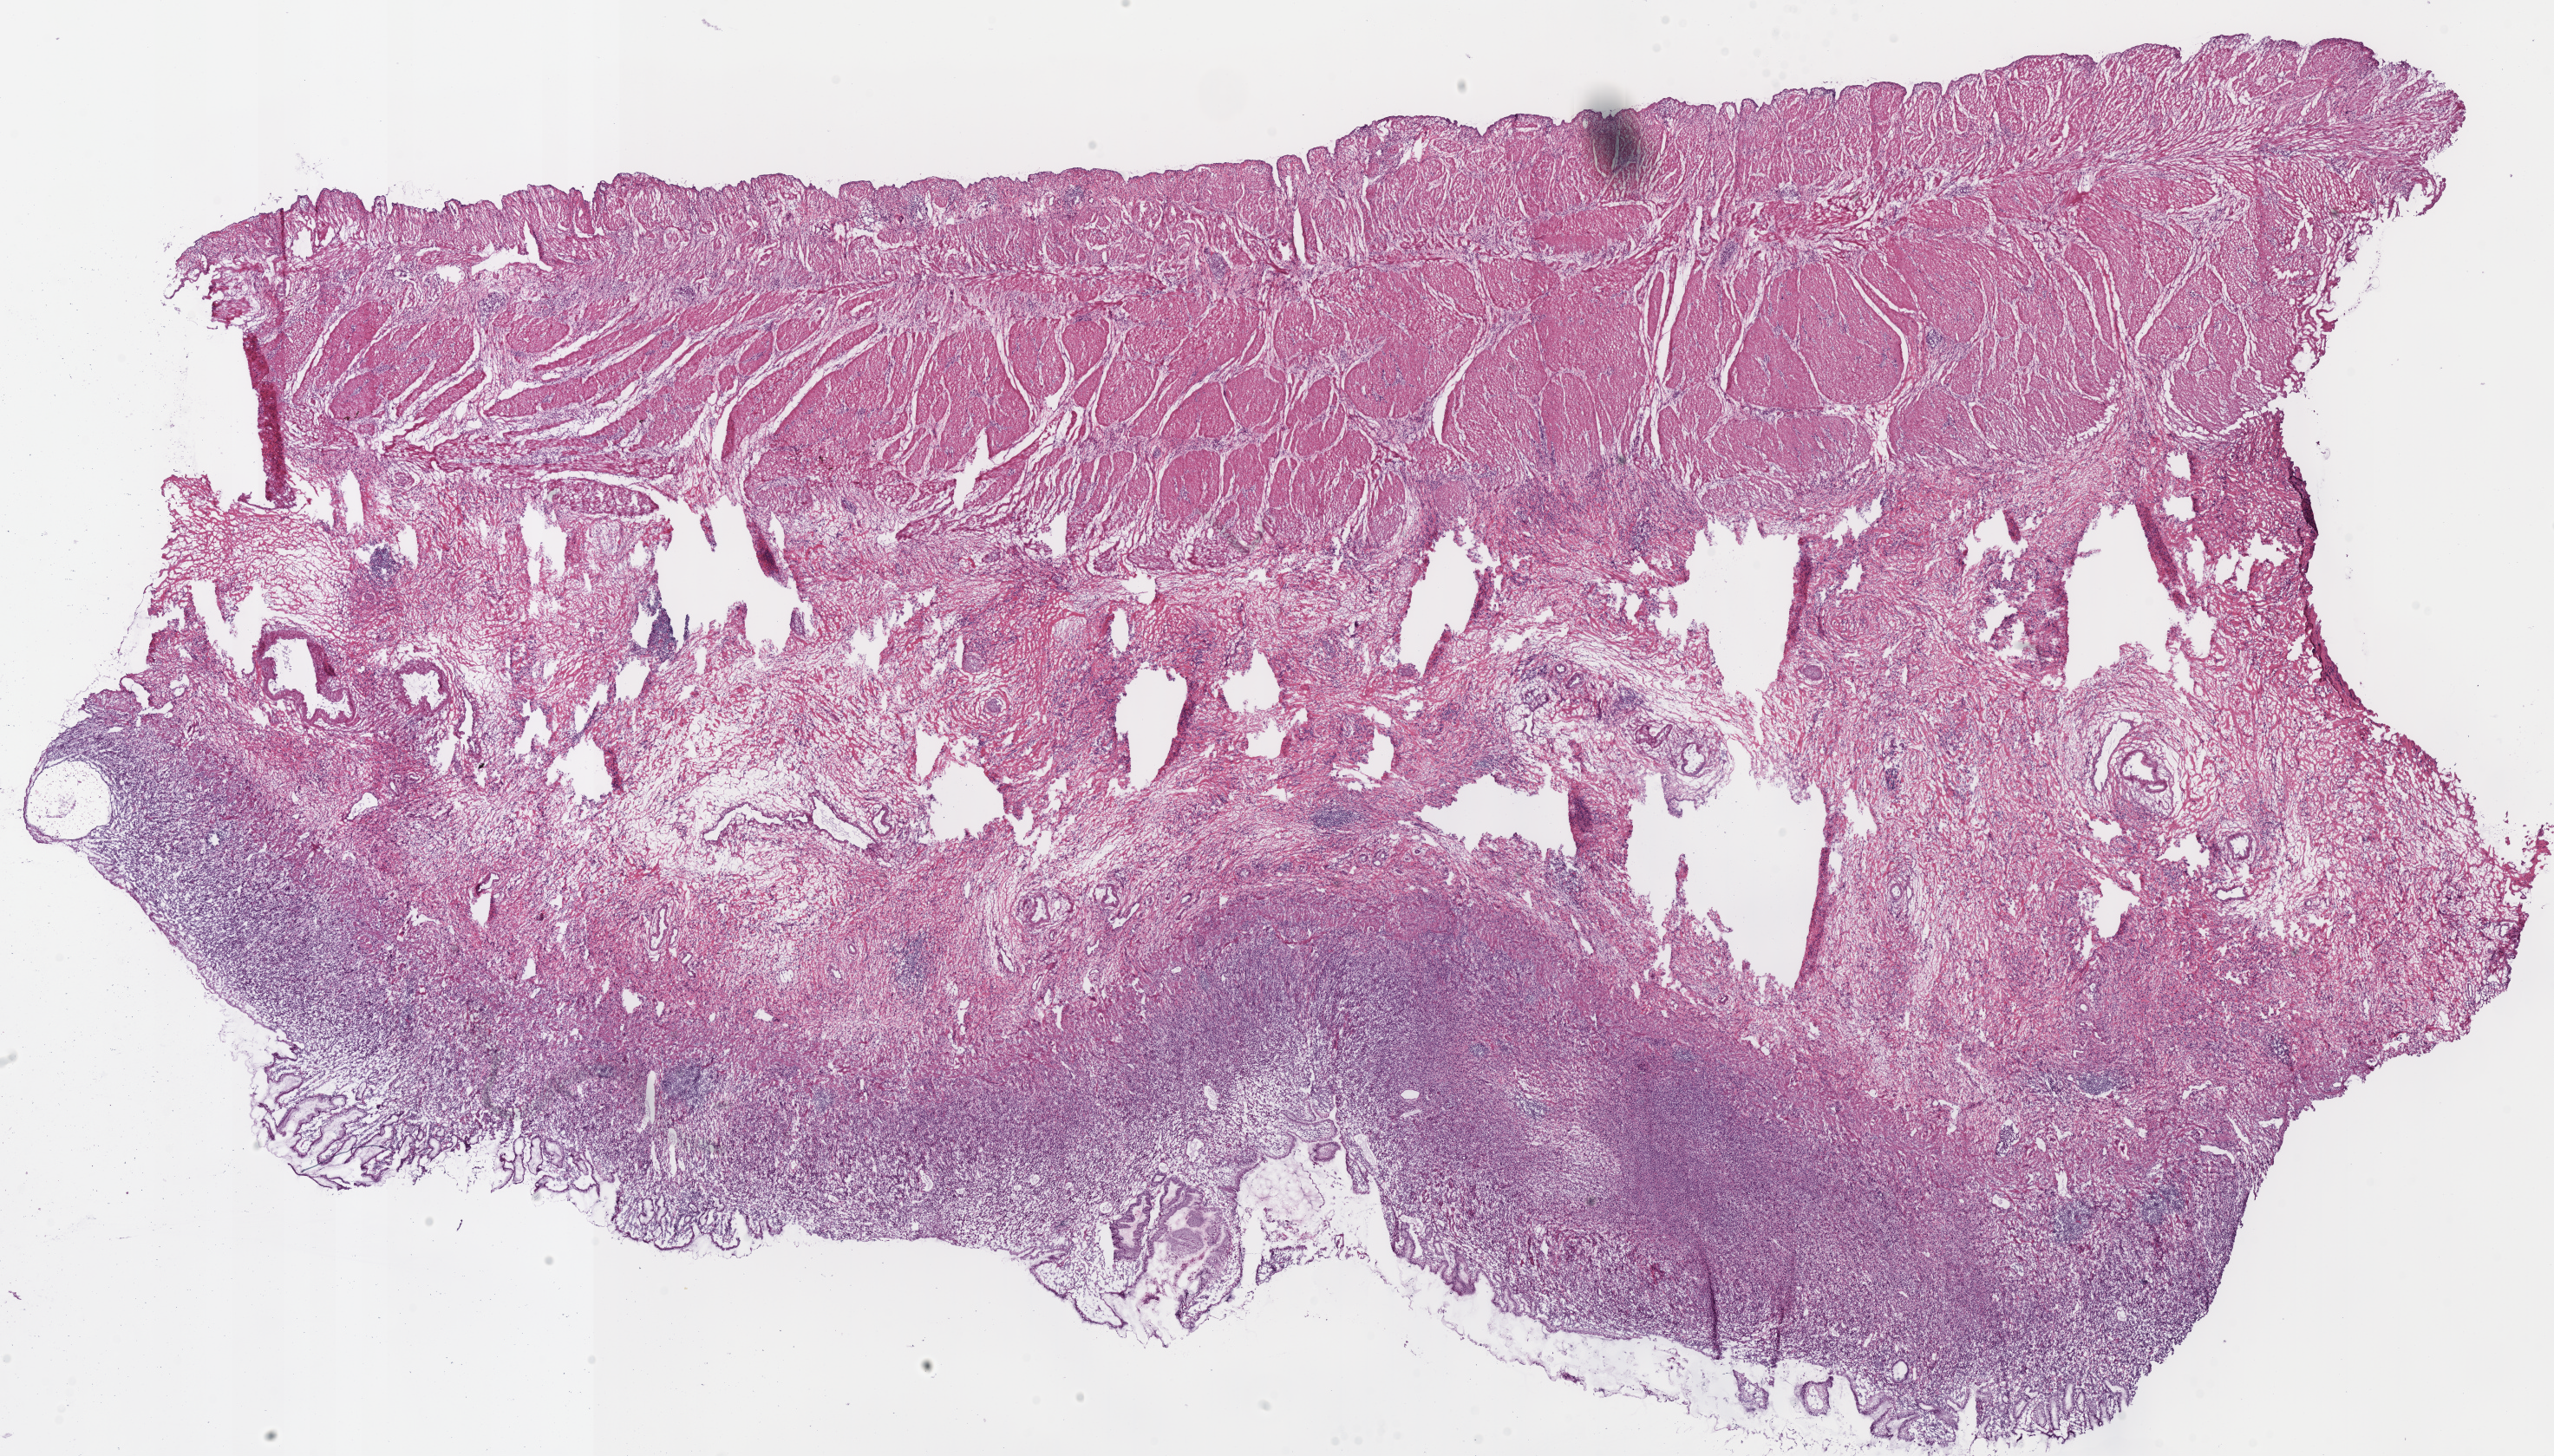
Digitized H&E-stained tissue section (whole slide), a low-resolution overview of the entire scanned area, about 23.2 x 13.2 mm. Frozen section. Sample: primary tumour, stomach. Patient: female, age at initial diagnosis 70 years. Histologic grade: G3 (poorly differentiated). Slide review estimates, as recorded: tumour cells 45%, tumour nuclei 60%, normal cells 15%, stromal cells 40%, necrosis 0%.
• lymph nodes positive (case pathology): 0 of 15 examined
• pathologic diagnosis: Adenocarcinoma, NOS (fundus of stomach)
• AJCC pathologic stage: IIA (7th edition)